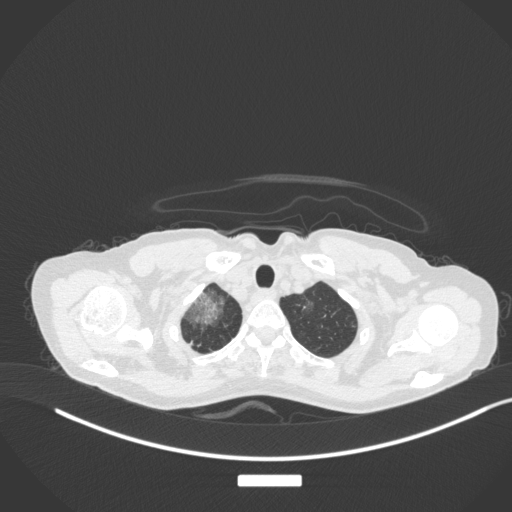
Chest CT, one axial slice. Reconstruction kernel B31f. 120 kVp. Lung window (W 1500 / L -600 HU). 1 mm slice thickness. 512 × 512 image matrix, field of view 400 × 400 mm. Patient: female, 59 years. From the clinical record (not read from this slice): clinical TNM (as recorded): T3 N0 M0; histopathological grade: G1.
Outlined on this slice (bounding box drawn by a radiologist):
- lung tumour (recorded histology: adenocarcinoma): bounding box [x1, y1, x2, y2] px = [181, 287, 227, 323]